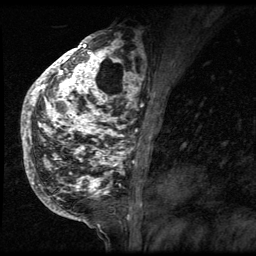
Breast MRI (dynamic contrast-enhanced), one sagittal slice; 3 images stored at this slice position (order not interpretable as contrast timing); 1.5 T; TE 4.2 ms, TR 9 ms; 2.5 mm slice thickness; 256 × 256 image matrix, field of view 180 × 180 mm. Patient: female, 50 years. Case-level facts recorded for this patient, not image findings: setting: breast cancer imaged before/during neoadjuvant chemotherapy; receptor status: triple-negative.
Outlined on this slice (semi-automatically segmented with operator editing):
- analysis volume of interest (the breast-tissue region the enhancement analysis was run in; not a lesion): box from (x=24, y=39) to (x=140, y=212) px
- tumour enhancement mask (voxels above the 140 % enhancement threshold inside the analysis volume of interest): (x=24, y=39)–(x=140, y=208)